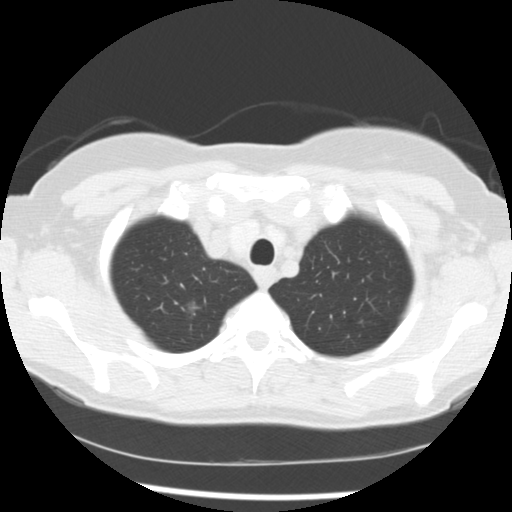
Chest CT (low-dose screening protocol), one axial image; baseline annual screen; lung window (W 1500 / L -600 HU); 2.5 mm slice thickness; slice 26 of 241 in the series; 512 × 512 image matrix. Female participant, aged 60 years at enrolment. Former smoker at enrolment.
• Lesion marked by an expert reader, bounding box [x1, y1, x2, y2] px = [165, 289, 215, 332].
• The screening reader recorded 3 non-calcified nodules or masses ≥4 mm on this exam (right upper lobe, right middle lobe, left lower lobe); which of them this box marks is not recorded.